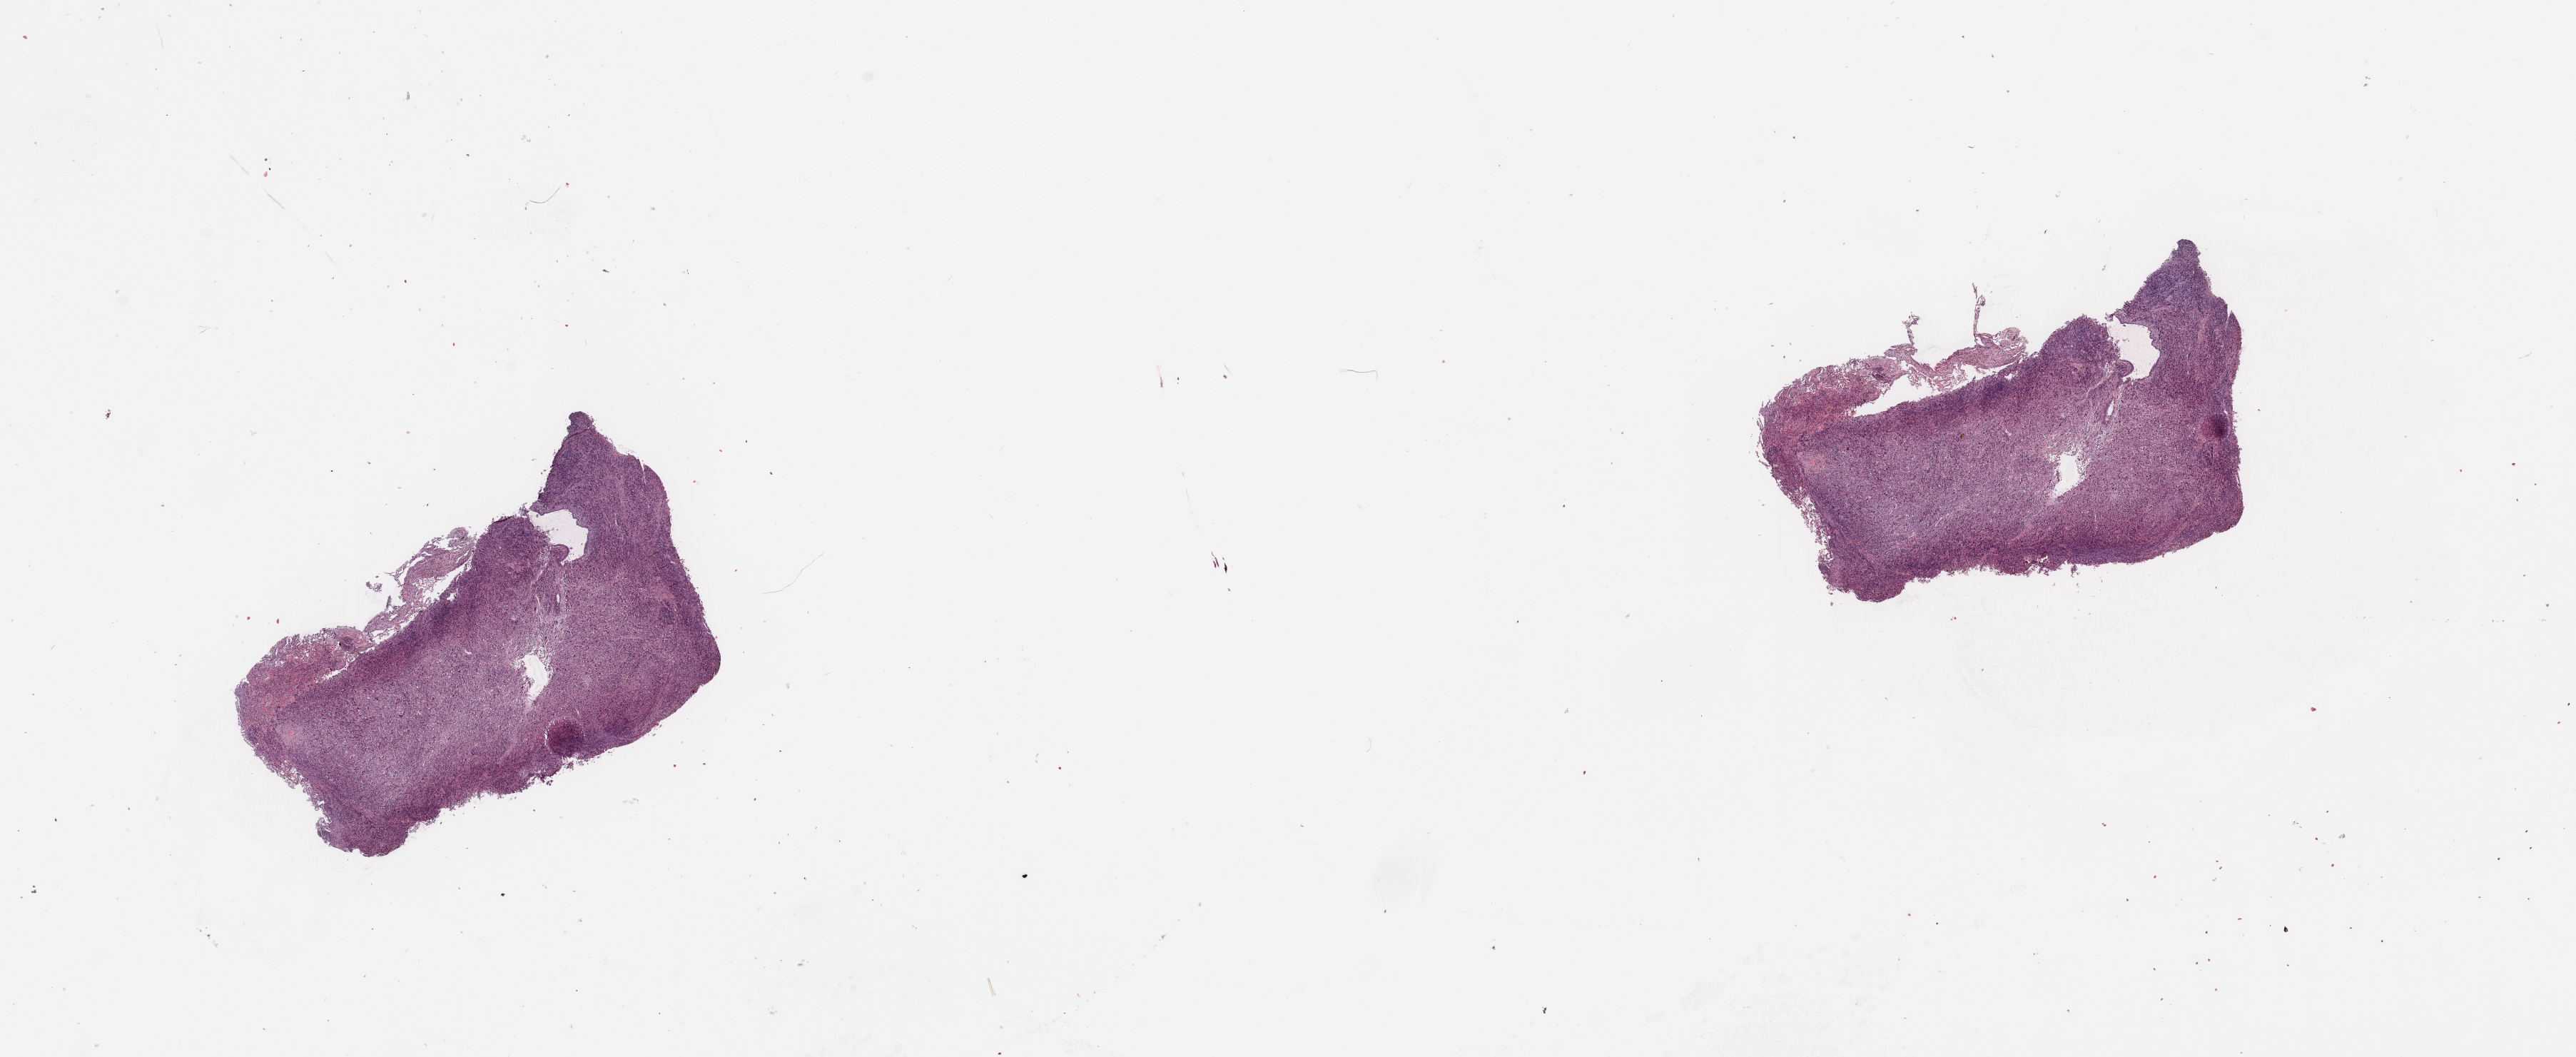
H&E-stained whole-slide image — whole scanned area (about 28.5 x 11.7 mm) shown as a low-resolution overview, tumour tissue sample, sampled site: lung. 64-year-old male patient. Histologic grade: G3 (poorly differentiated). Composition of this section per pathologist review: tumour nuclei 85%, necrosis 5%.
• AJCC pathologic stage: IA1
• histologic diagnosis: Adenocarcinoma, NOS